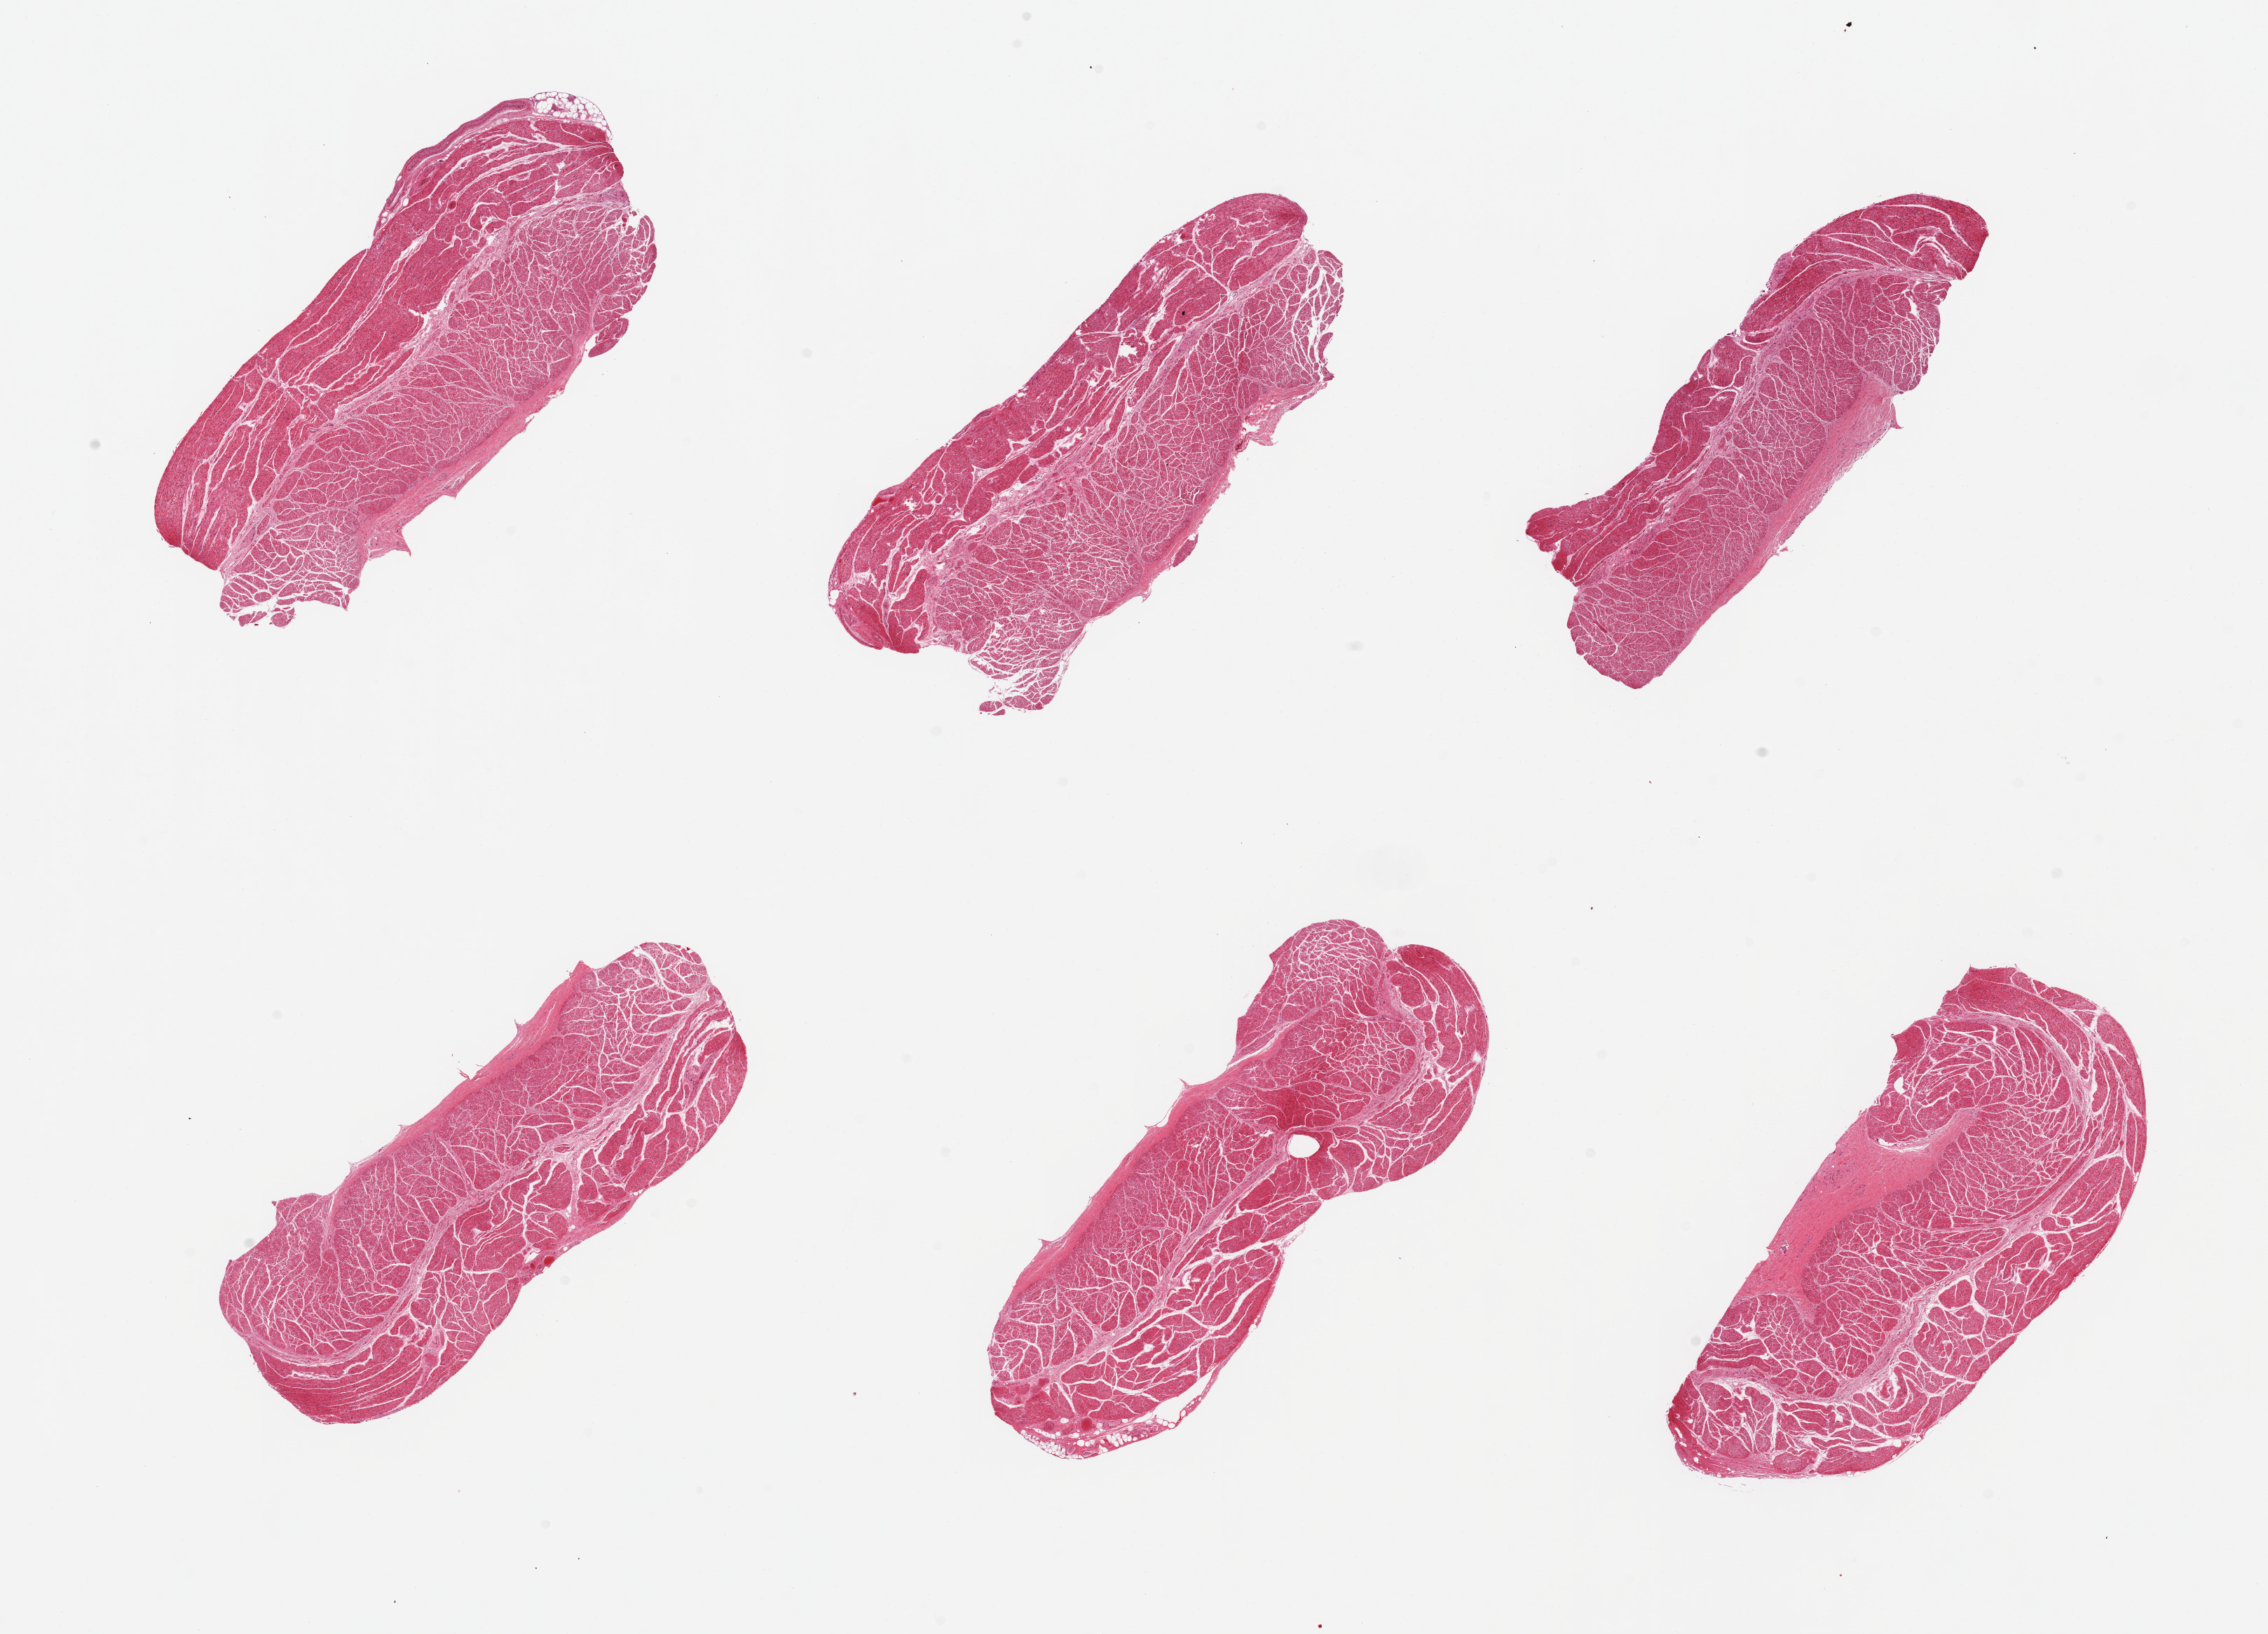
Whole-slide image, haematoxylin and eosin stain — a low-resolution overview of the entire scanned area, about 25.6 x 18.4 mm, PAXgene-fixed paraffin-embedded (PFPE) section, sampled site (target tissue): esophageal muscle, tissue donor sample. Donor sex: male.
Review note (as recorded): 6 pieces; well trimmed.